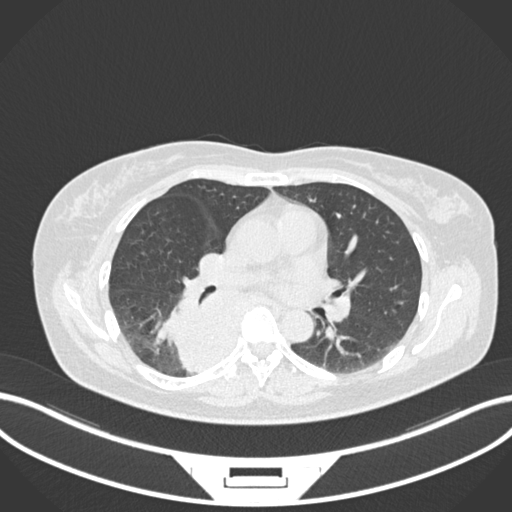
Chest CT, one axial slice. Position 596 of 677 along the scan axis. Reconstruction kernel B30f. Lung window (W 1500 / L -600 HU). 1 mm slice thickness. 512 × 512 image matrix, field of view 400 × 400 mm. Patient: female, 54 years. Case-level facts recorded for this patient, not image findings: clinical TNM (as recorded): T4 N0 M0.
Outlined on this slice (bounding box drawn by a radiologist):
- lung tumour (recorded histology: adenocarcinoma): bounding box <162,277,254,380> (left, top, right, bottom; pixels)